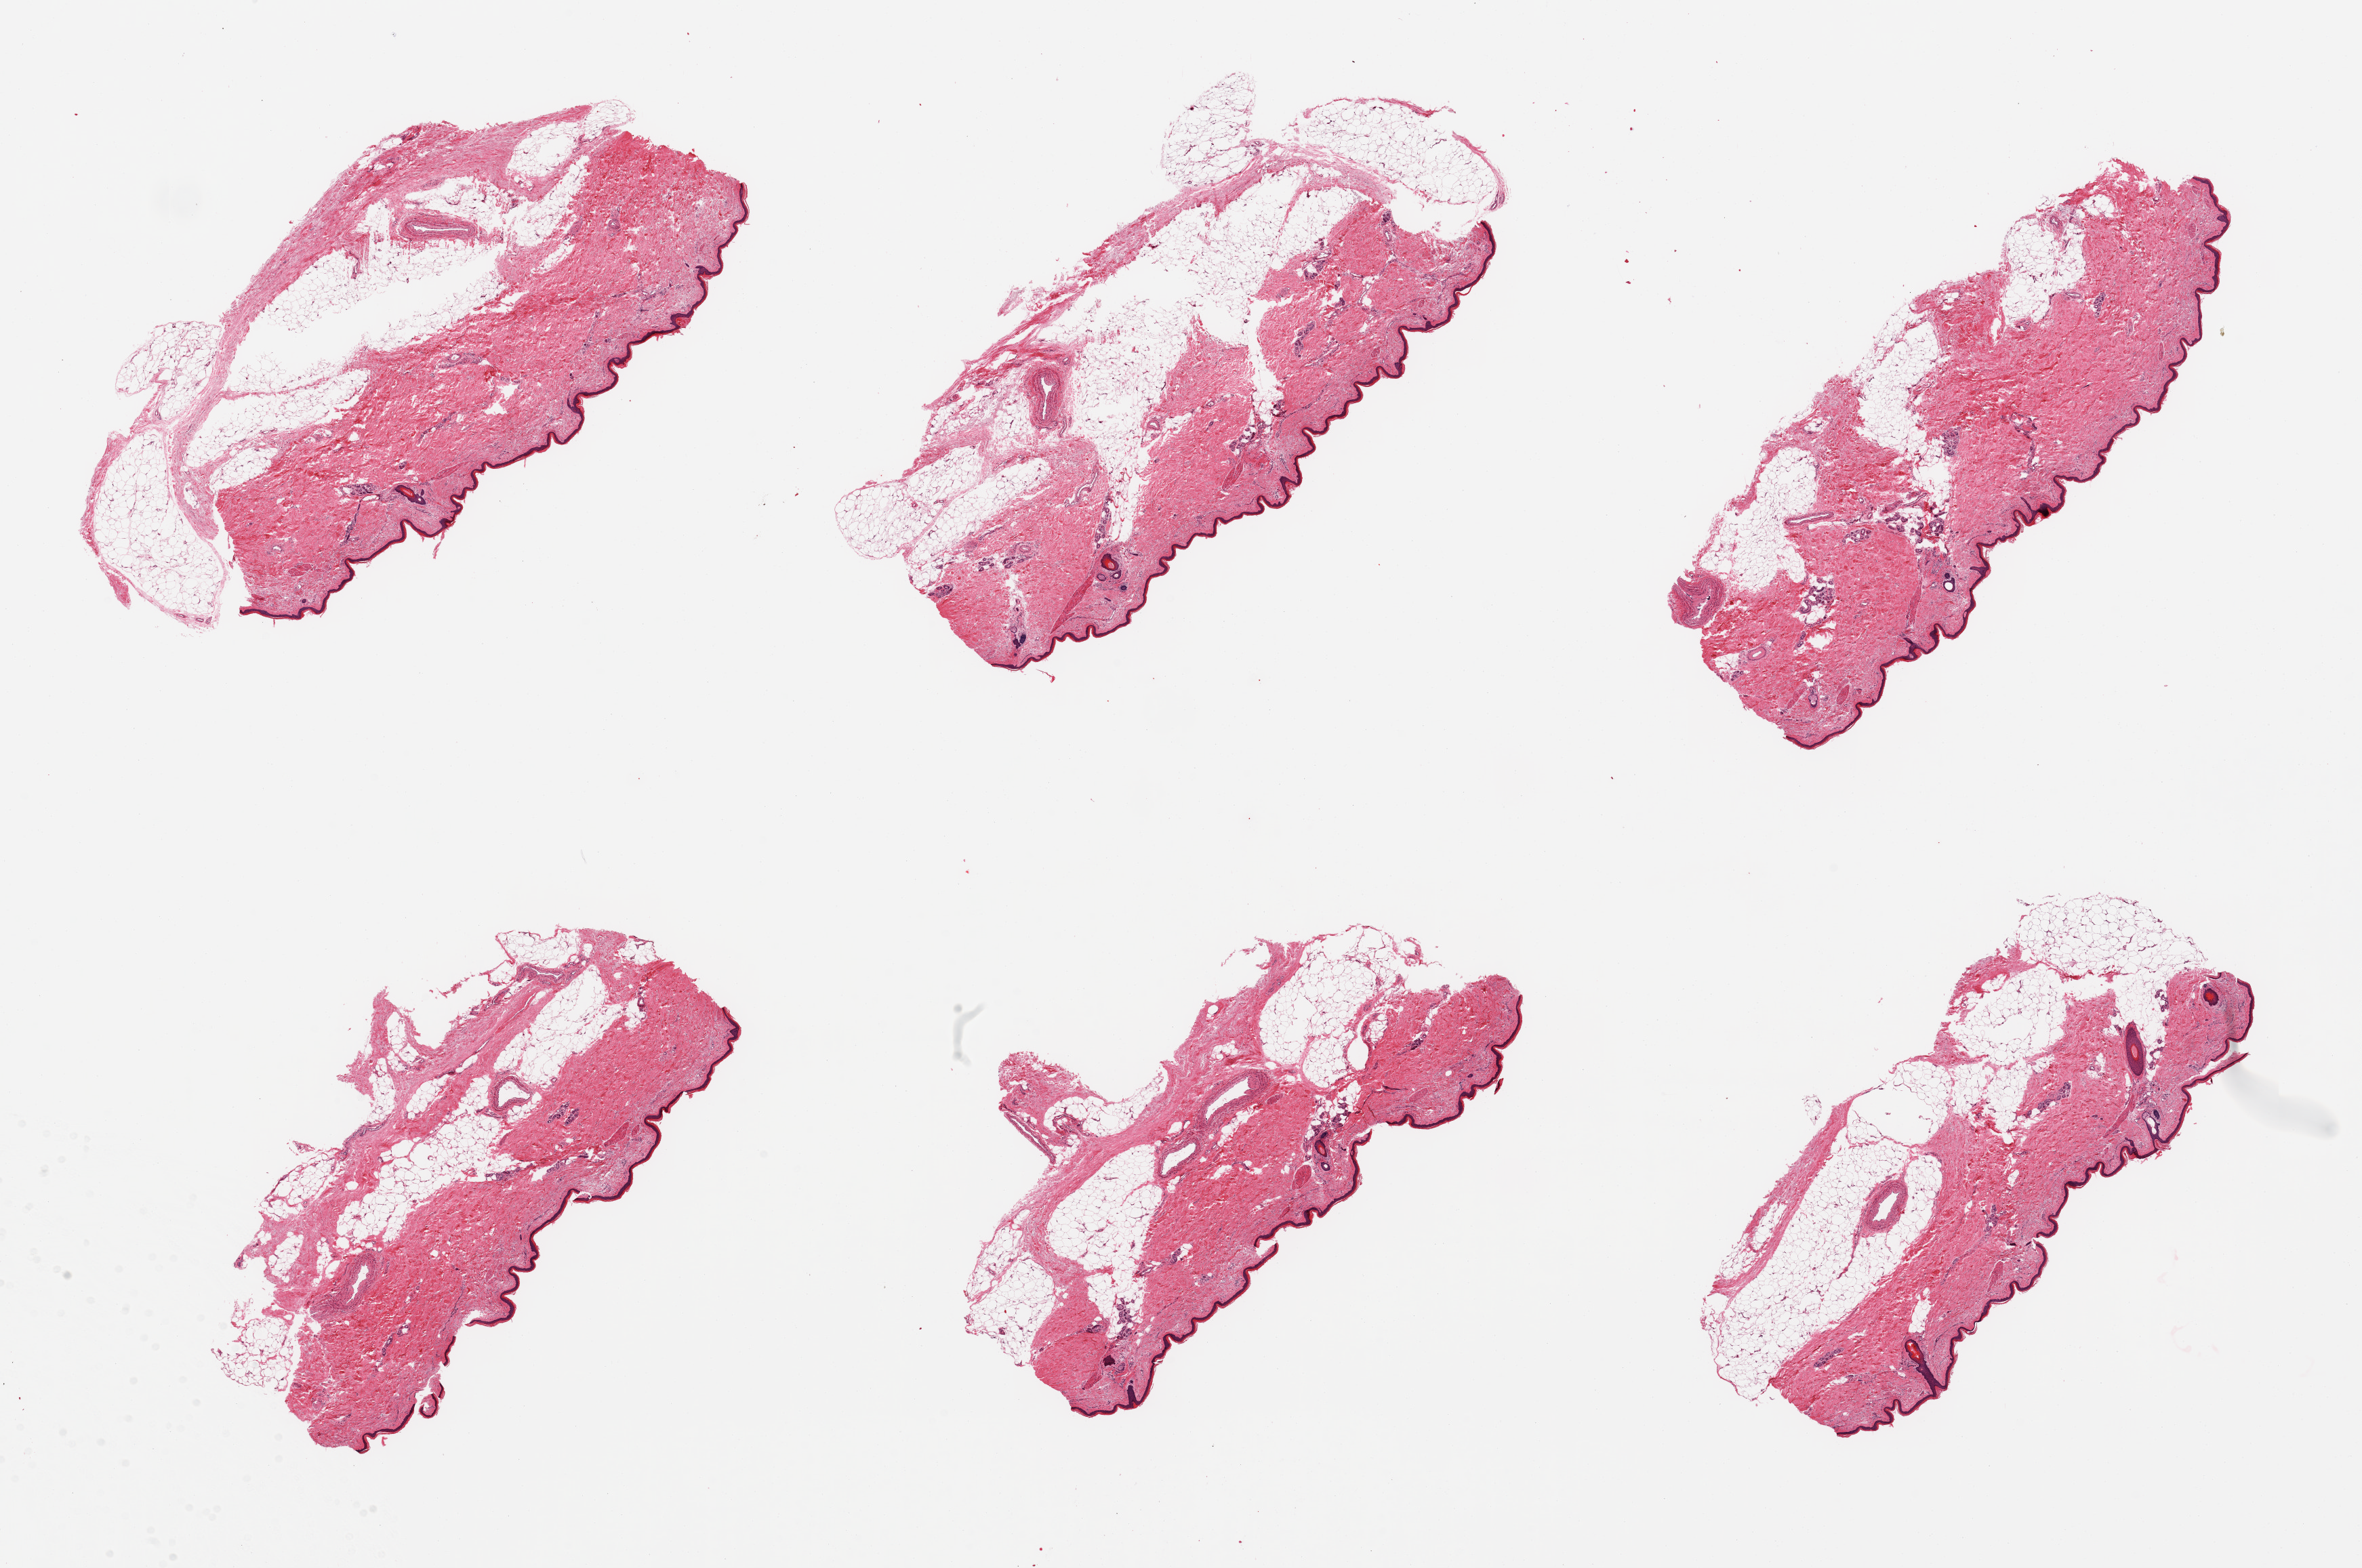
Hematoxylin and eosin (H&E) whole-slide image — shown as a low-resolution overview of the whole scanned area (about 27.6 x 18.3 mm, acquisition: 20x scan), PAXgene-fixed paraffin-embedded (PFPE) section, section of skin of lower leg (target tissue), donor tissue sample. Male donor.
Reviewer comment on this tissue sample: 6 pieces; excessive subcutaneous fat included in sample; makes up 50% of area.